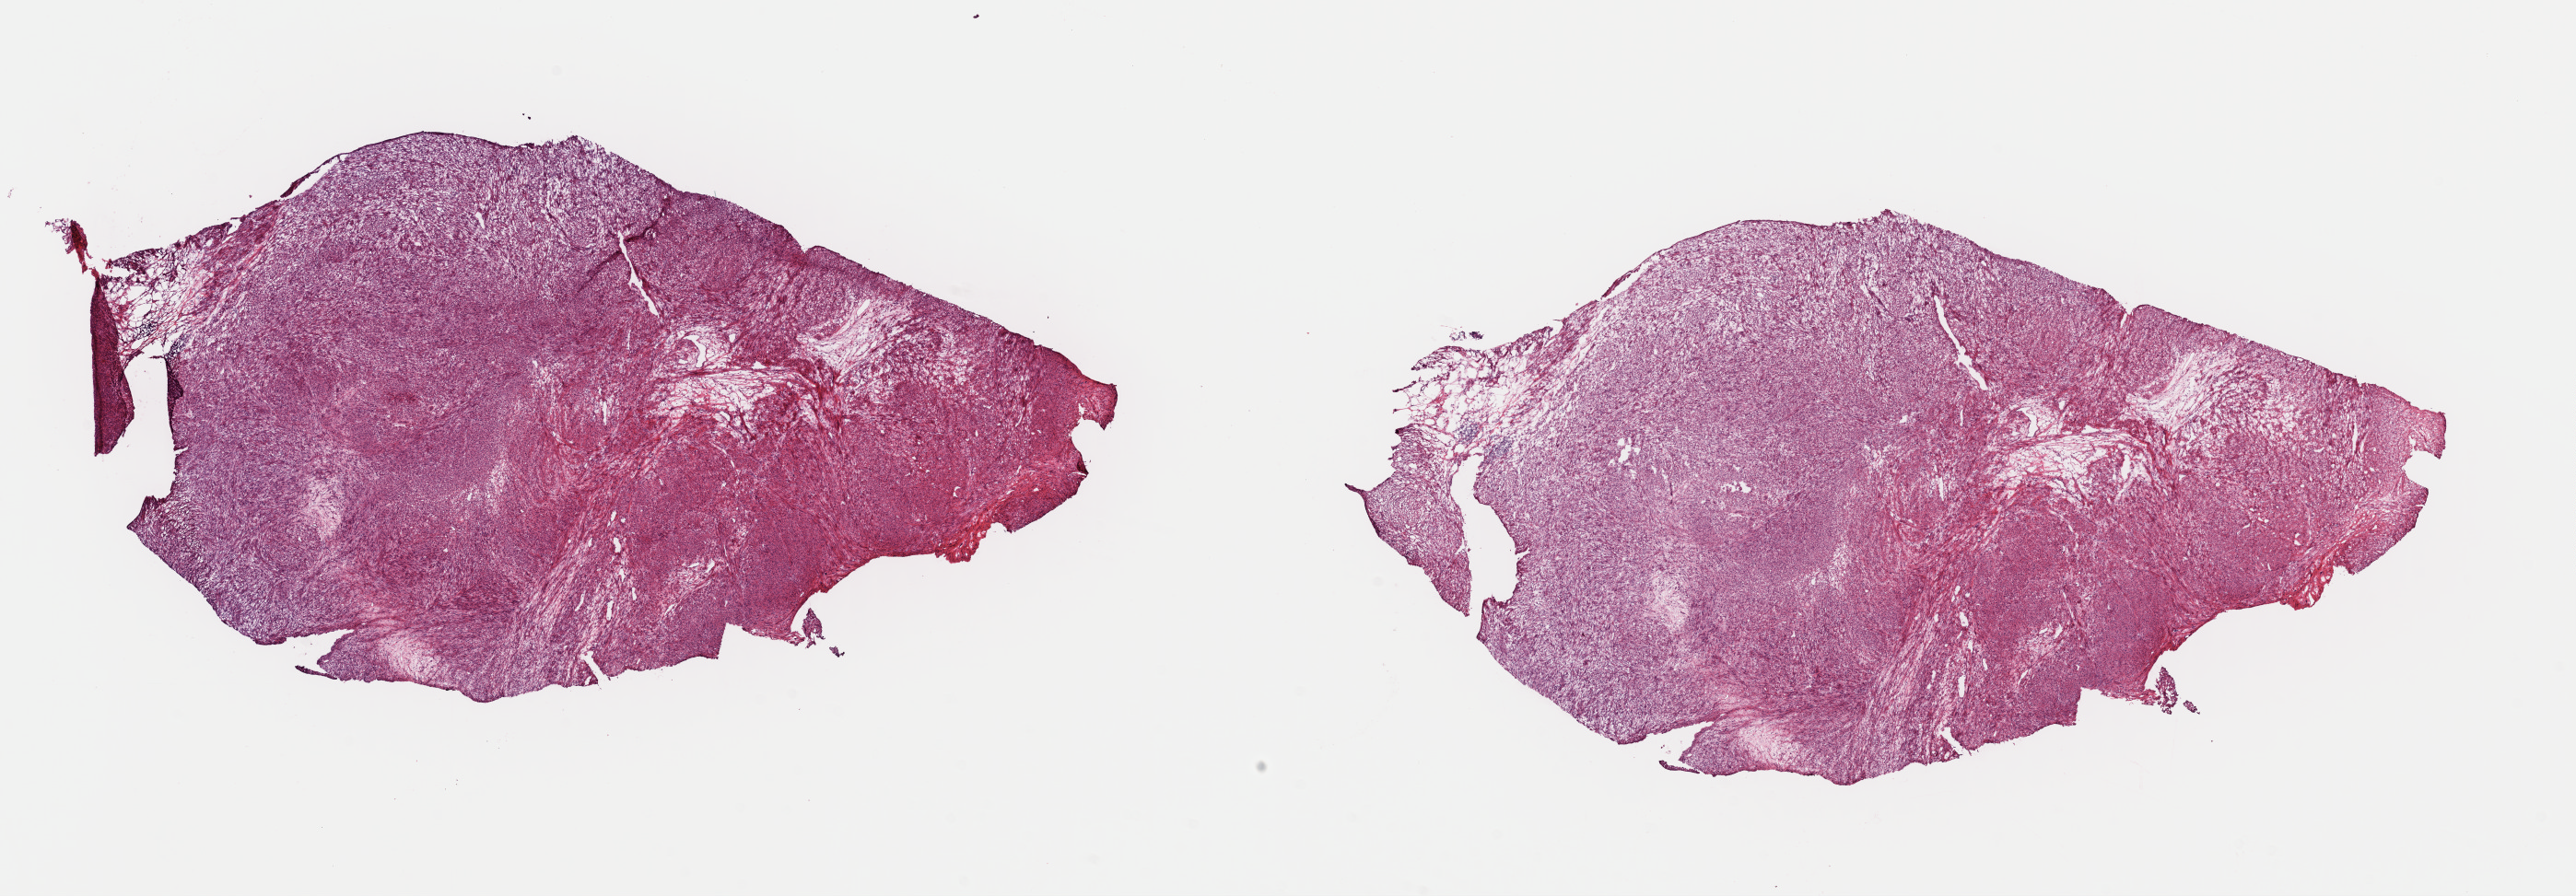
H&E-stained whole-slide image — low-resolution overview of the scanned area, about 22.1 x 7.7 mm (acquisition: 40x scan). Frozen section from the top of the tissue portion. Primary tumour sample from the retroperitoneum and peritoneum. Male patient; age at initial diagnosis 61 years. Pathologist review of this section (percent, as recorded): tumour cells 100%, tumour nuclei 85%, normal cells 0%, stromal cells 0%, necrosis 0%. Inflammatory infiltration, as recorded: lymphocyte infiltration 1%, monocyte infiltration 0%, neutrophil infiltration 0%.
- histologic diagnosis: Leiomyosarcoma, NOS (retroperitoneum)